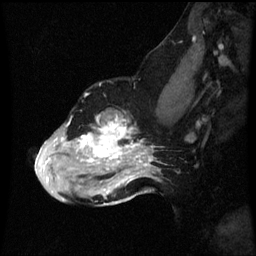
Breast MRI (dynamic contrast-enhanced), one sagittal slice; dynamic contrast-enhanced series, image 2 of 3 at this slice position (ordered by acquisition); 1.5 T; TE 4.2 ms, TR 8.9 ms; 2 mm slice thickness; 256 × 256 image matrix. Female patient, age 49 years. From the clinical record (not read from this slice): setting: breast cancer imaged before/during neoadjuvant chemotherapy; receptor status: HR-positive, HER2-negative.
Annotated regions visible in this slice (semi-automatic segmentation, software-assisted and operator-edited):
- analysis volume of interest (the breast-tissue region the enhancement analysis was run in; not a lesion): box from (x=36, y=110) to (x=159, y=199) px
- tumour enhancement mask (voxels above the 70 % enhancement threshold inside the analysis volume of interest): (x=38, y=116)–(x=153, y=183)